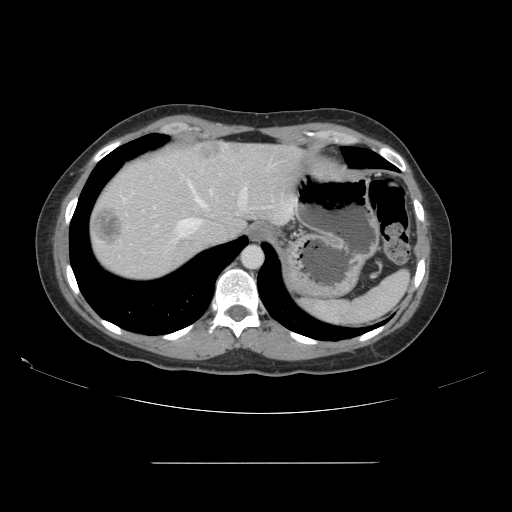
Contrast-enhanced abdominal CT, one axial slice; position 129 of 151 along the scan axis; 120 kVp; intravenous contrast given; soft-tissue window (W 400 / L 40 HU); 2.5 mm slice thickness; 512 × 512 image matrix, field of view 421 × 421 mm. Female patient, age 46 years. Case-level facts recorded for this patient, not image findings: diagnosis: colorectal cancer liver metastases, imaged before liver resection.
Structures marked on this image (outlined manually by an expert reader):
- hepatic veins: box from (x=124, y=181) to (x=248, y=240) px
- liver: (x=90, y=143)–(x=298, y=281)
- planned liver remnant (the part of the liver to remain after resection): (x=101, y=144)–(x=298, y=241)
- liver metastasis: (x=94, y=206)–(x=123, y=244)
- liver metastasis: (x=199, y=145)–(x=225, y=159)